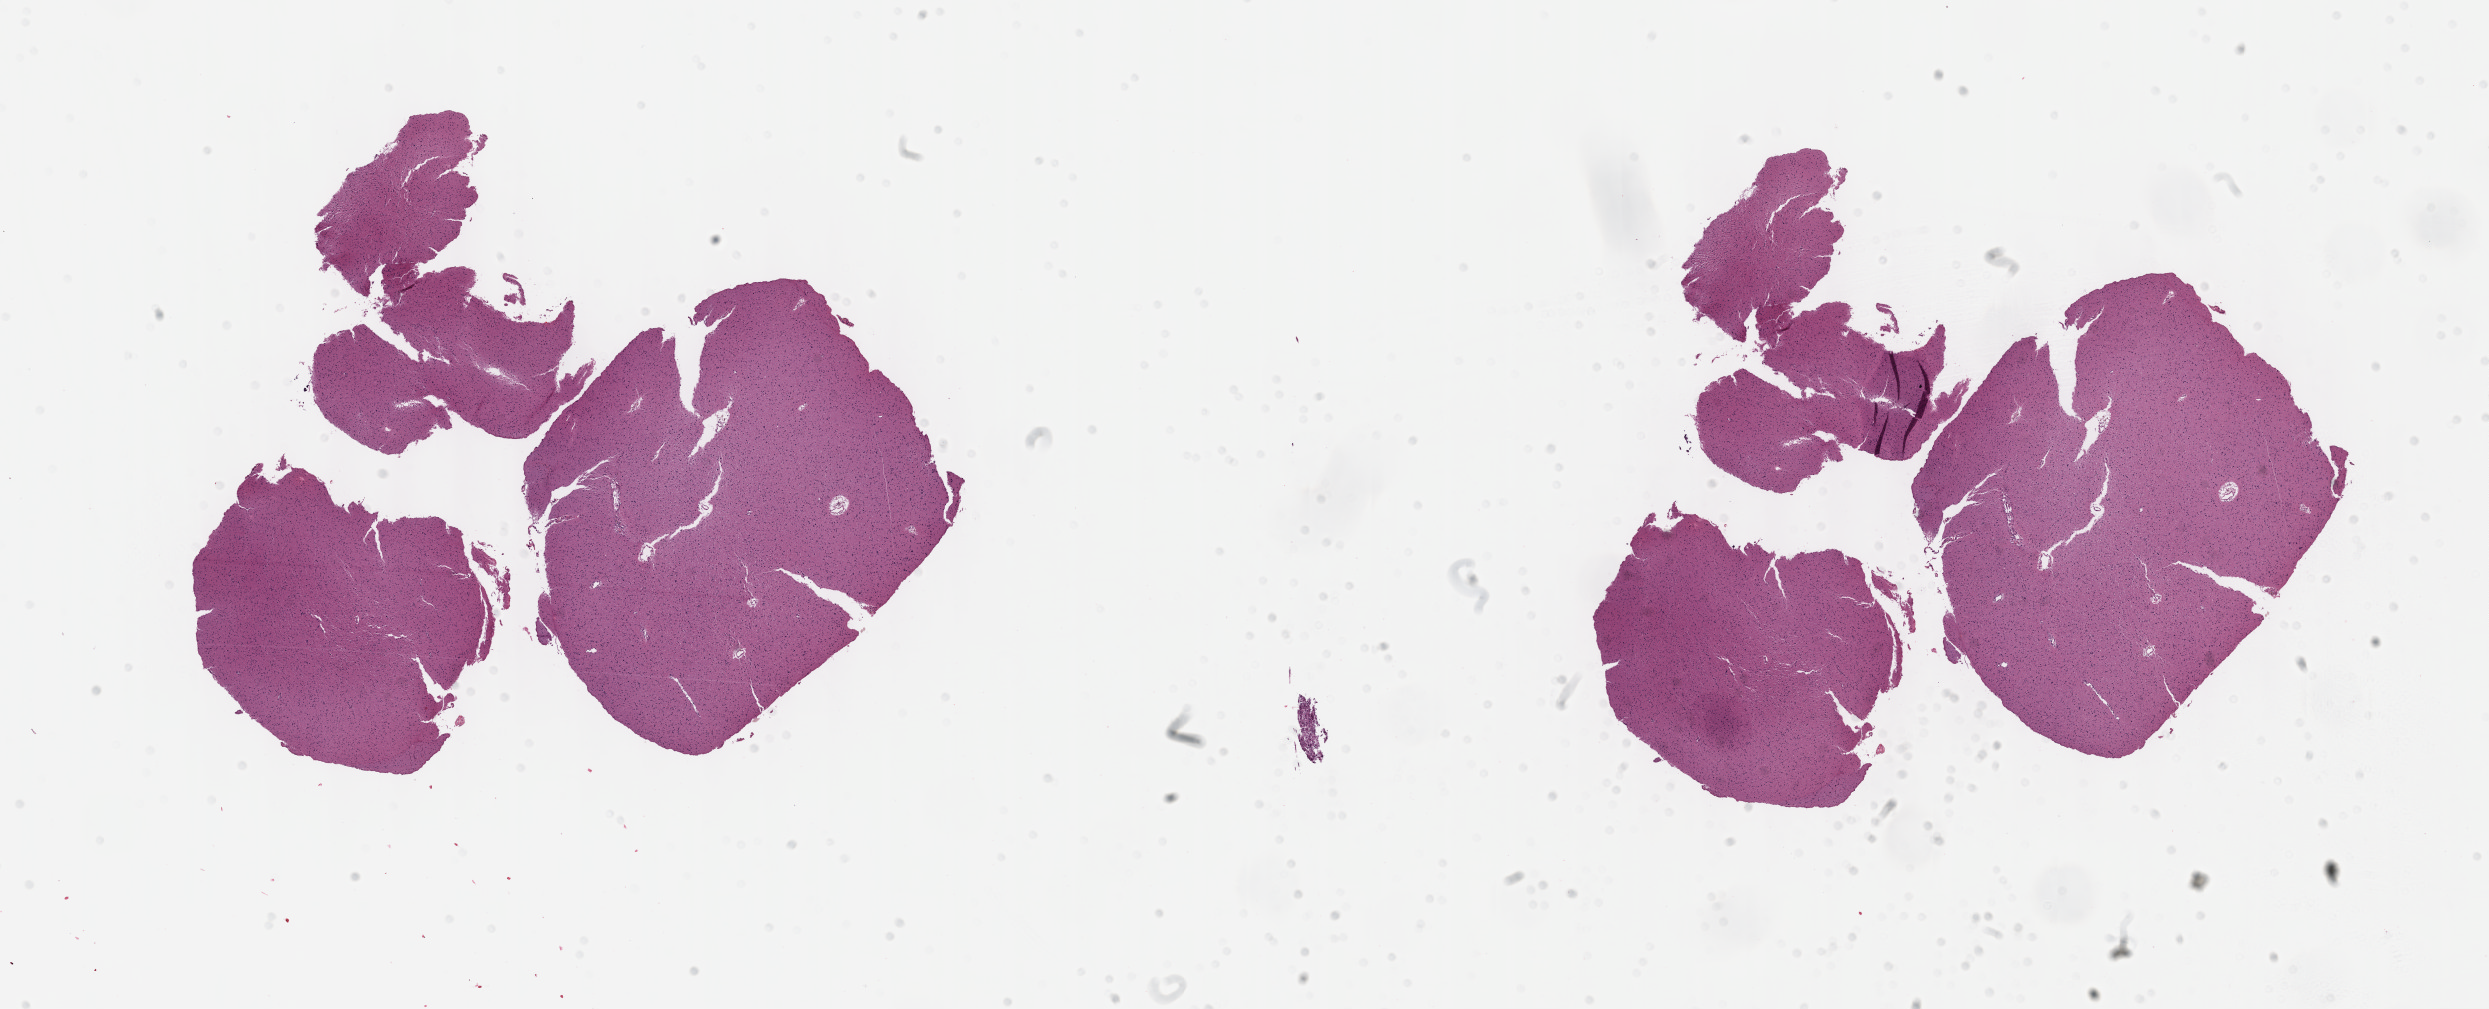
H&E whole-slide image, whole scanned area (about 20.1 x 8.2 mm, slide scanned at 40x) shown as a low-resolution overview; formalin-fixed paraffin-embedded (FFPE) diagnostic section; sample: primary tumour, brain. Female patient; age at initial diagnosis 30 years. Histologic grade: G2 (moderately differentiated).
Pathologic diagnosis: Mixed glioma (cerebrum). Laterality: right.